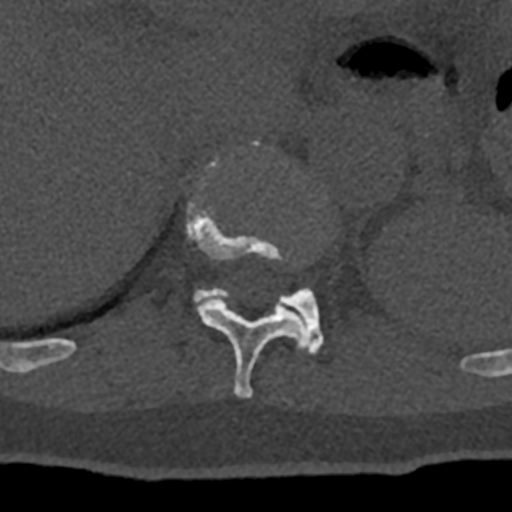
CT including the spine, one axial slice; position 529 of 797 along the scan axis; 120 kVp; bone window (W 1800 / L 400 HU); 512 × 512 image matrix. Male patient, age 74 years. Case-level facts recorded for this patient, not image findings: primary cancer: renal; vertebrae with lytic lesions (as recorded): T10, L1, L2, L3, L4, L5.
Annotated regions visible in this slice (semi-automatic segmentation, software-assisted and operator-edited):
- T11 vertebra: box from (x=70, y=141) to (x=308, y=398) px
- T12 vertebra: (x=193, y=287)–(x=323, y=354)